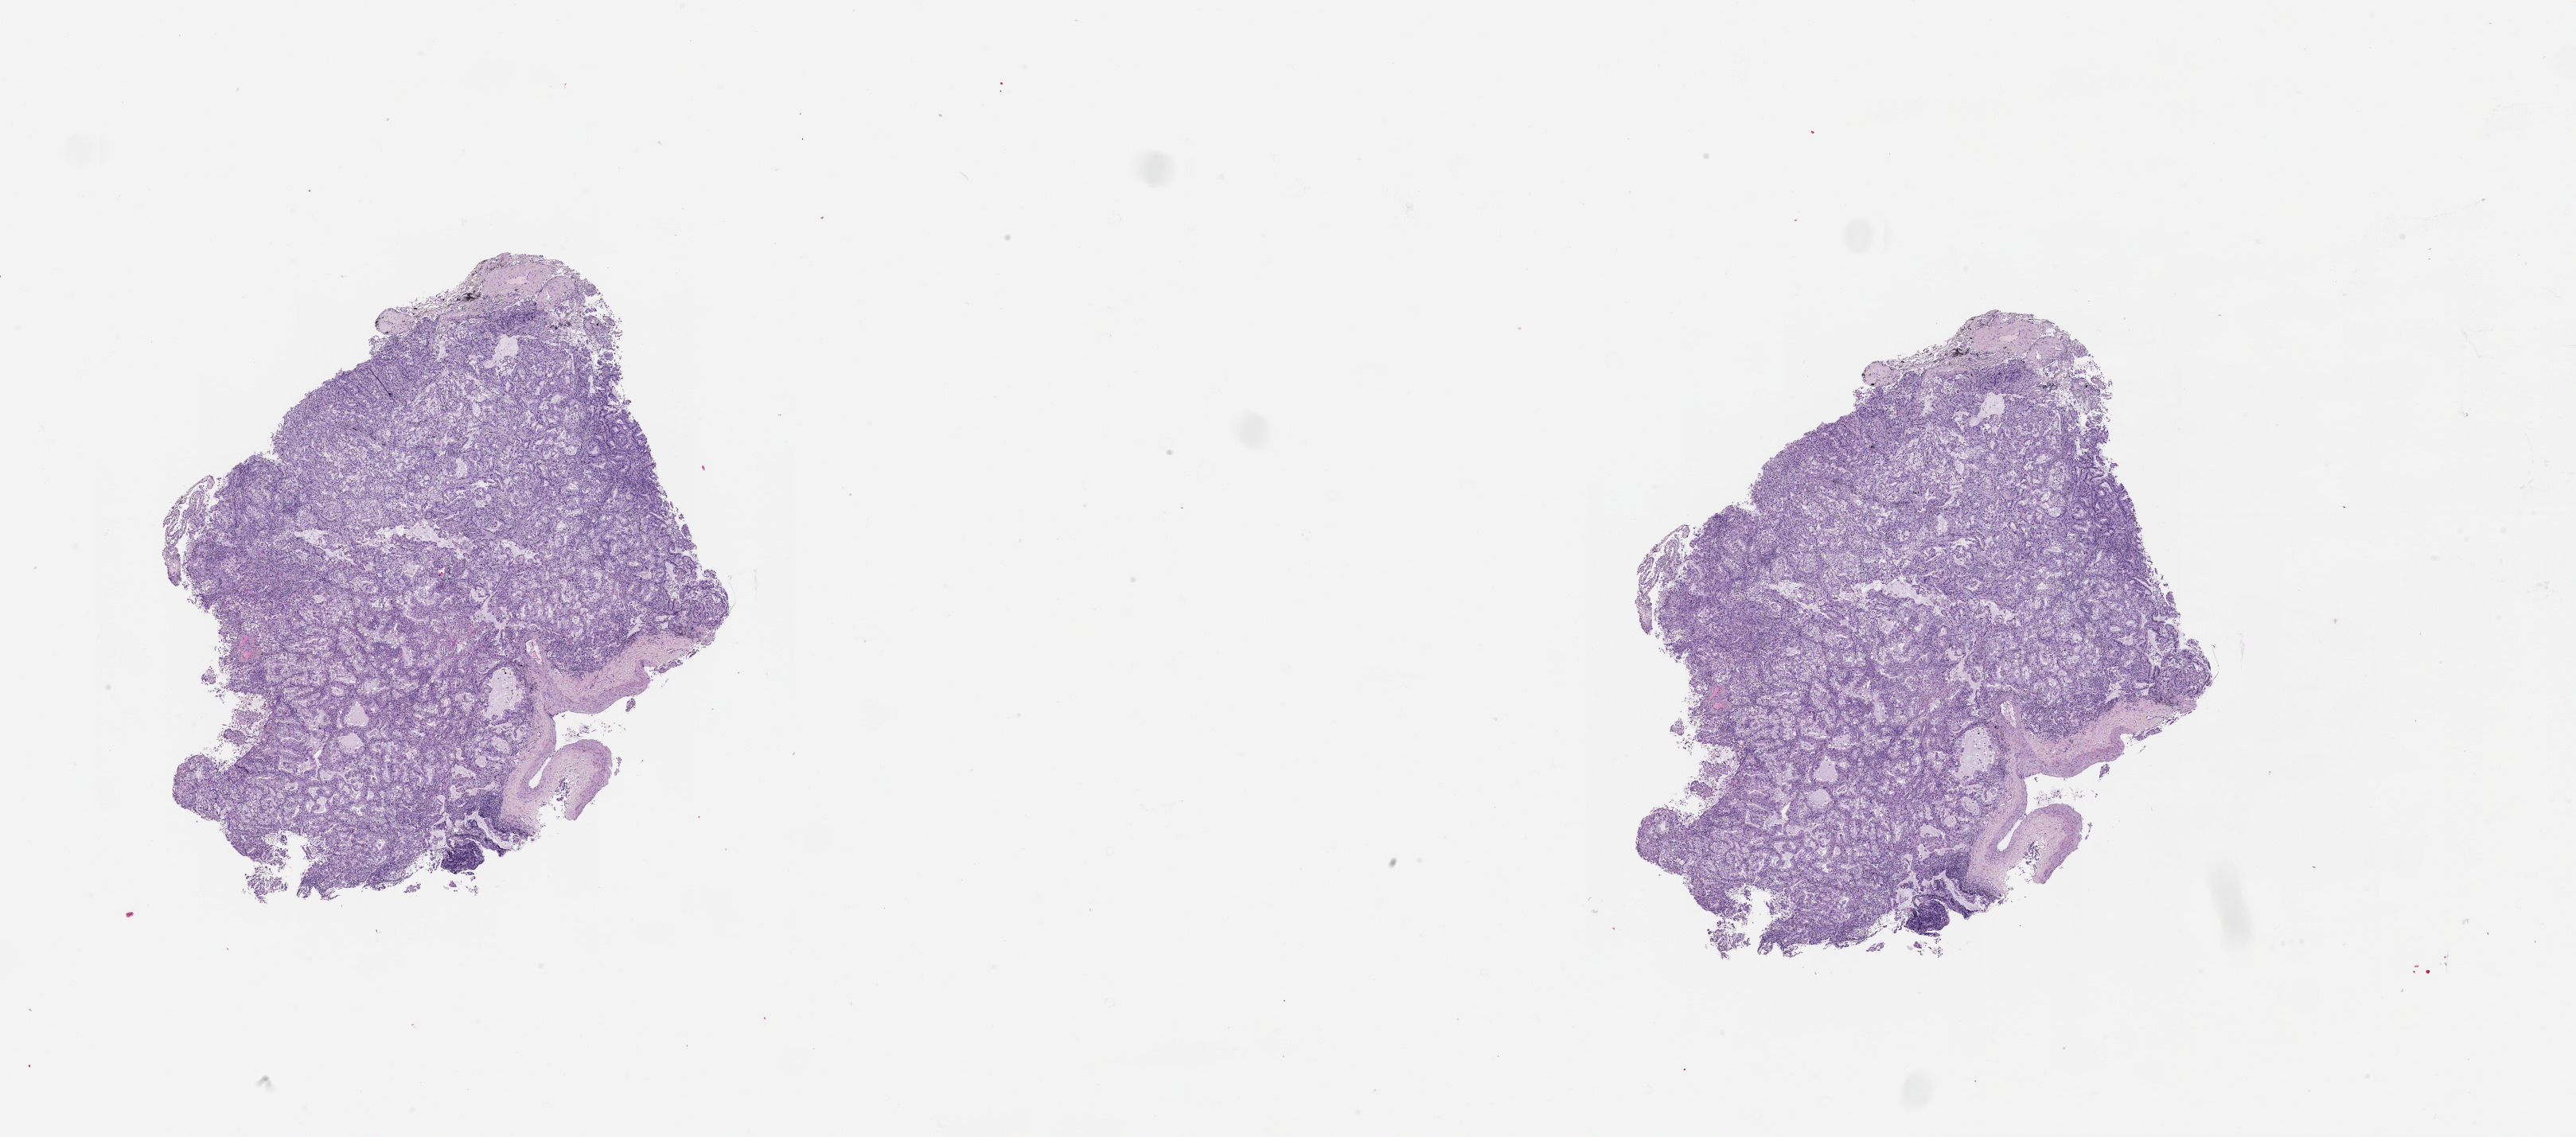
Digitized H&E tissue section (whole slide) — shown as a low-resolution overview of the whole scanned area (about 26.1 x 11.5 mm), tumour tissue sample, sampled site: lung. 67-year-old male patient. Histologic grade: G2 (moderately differentiated). Pathologist review of this section (percent, as recorded): tumour nuclei 70%, necrosis 5%.
Diagnosis: Adenocarcinoma, NOS. AJCC pathologic stage: IA.